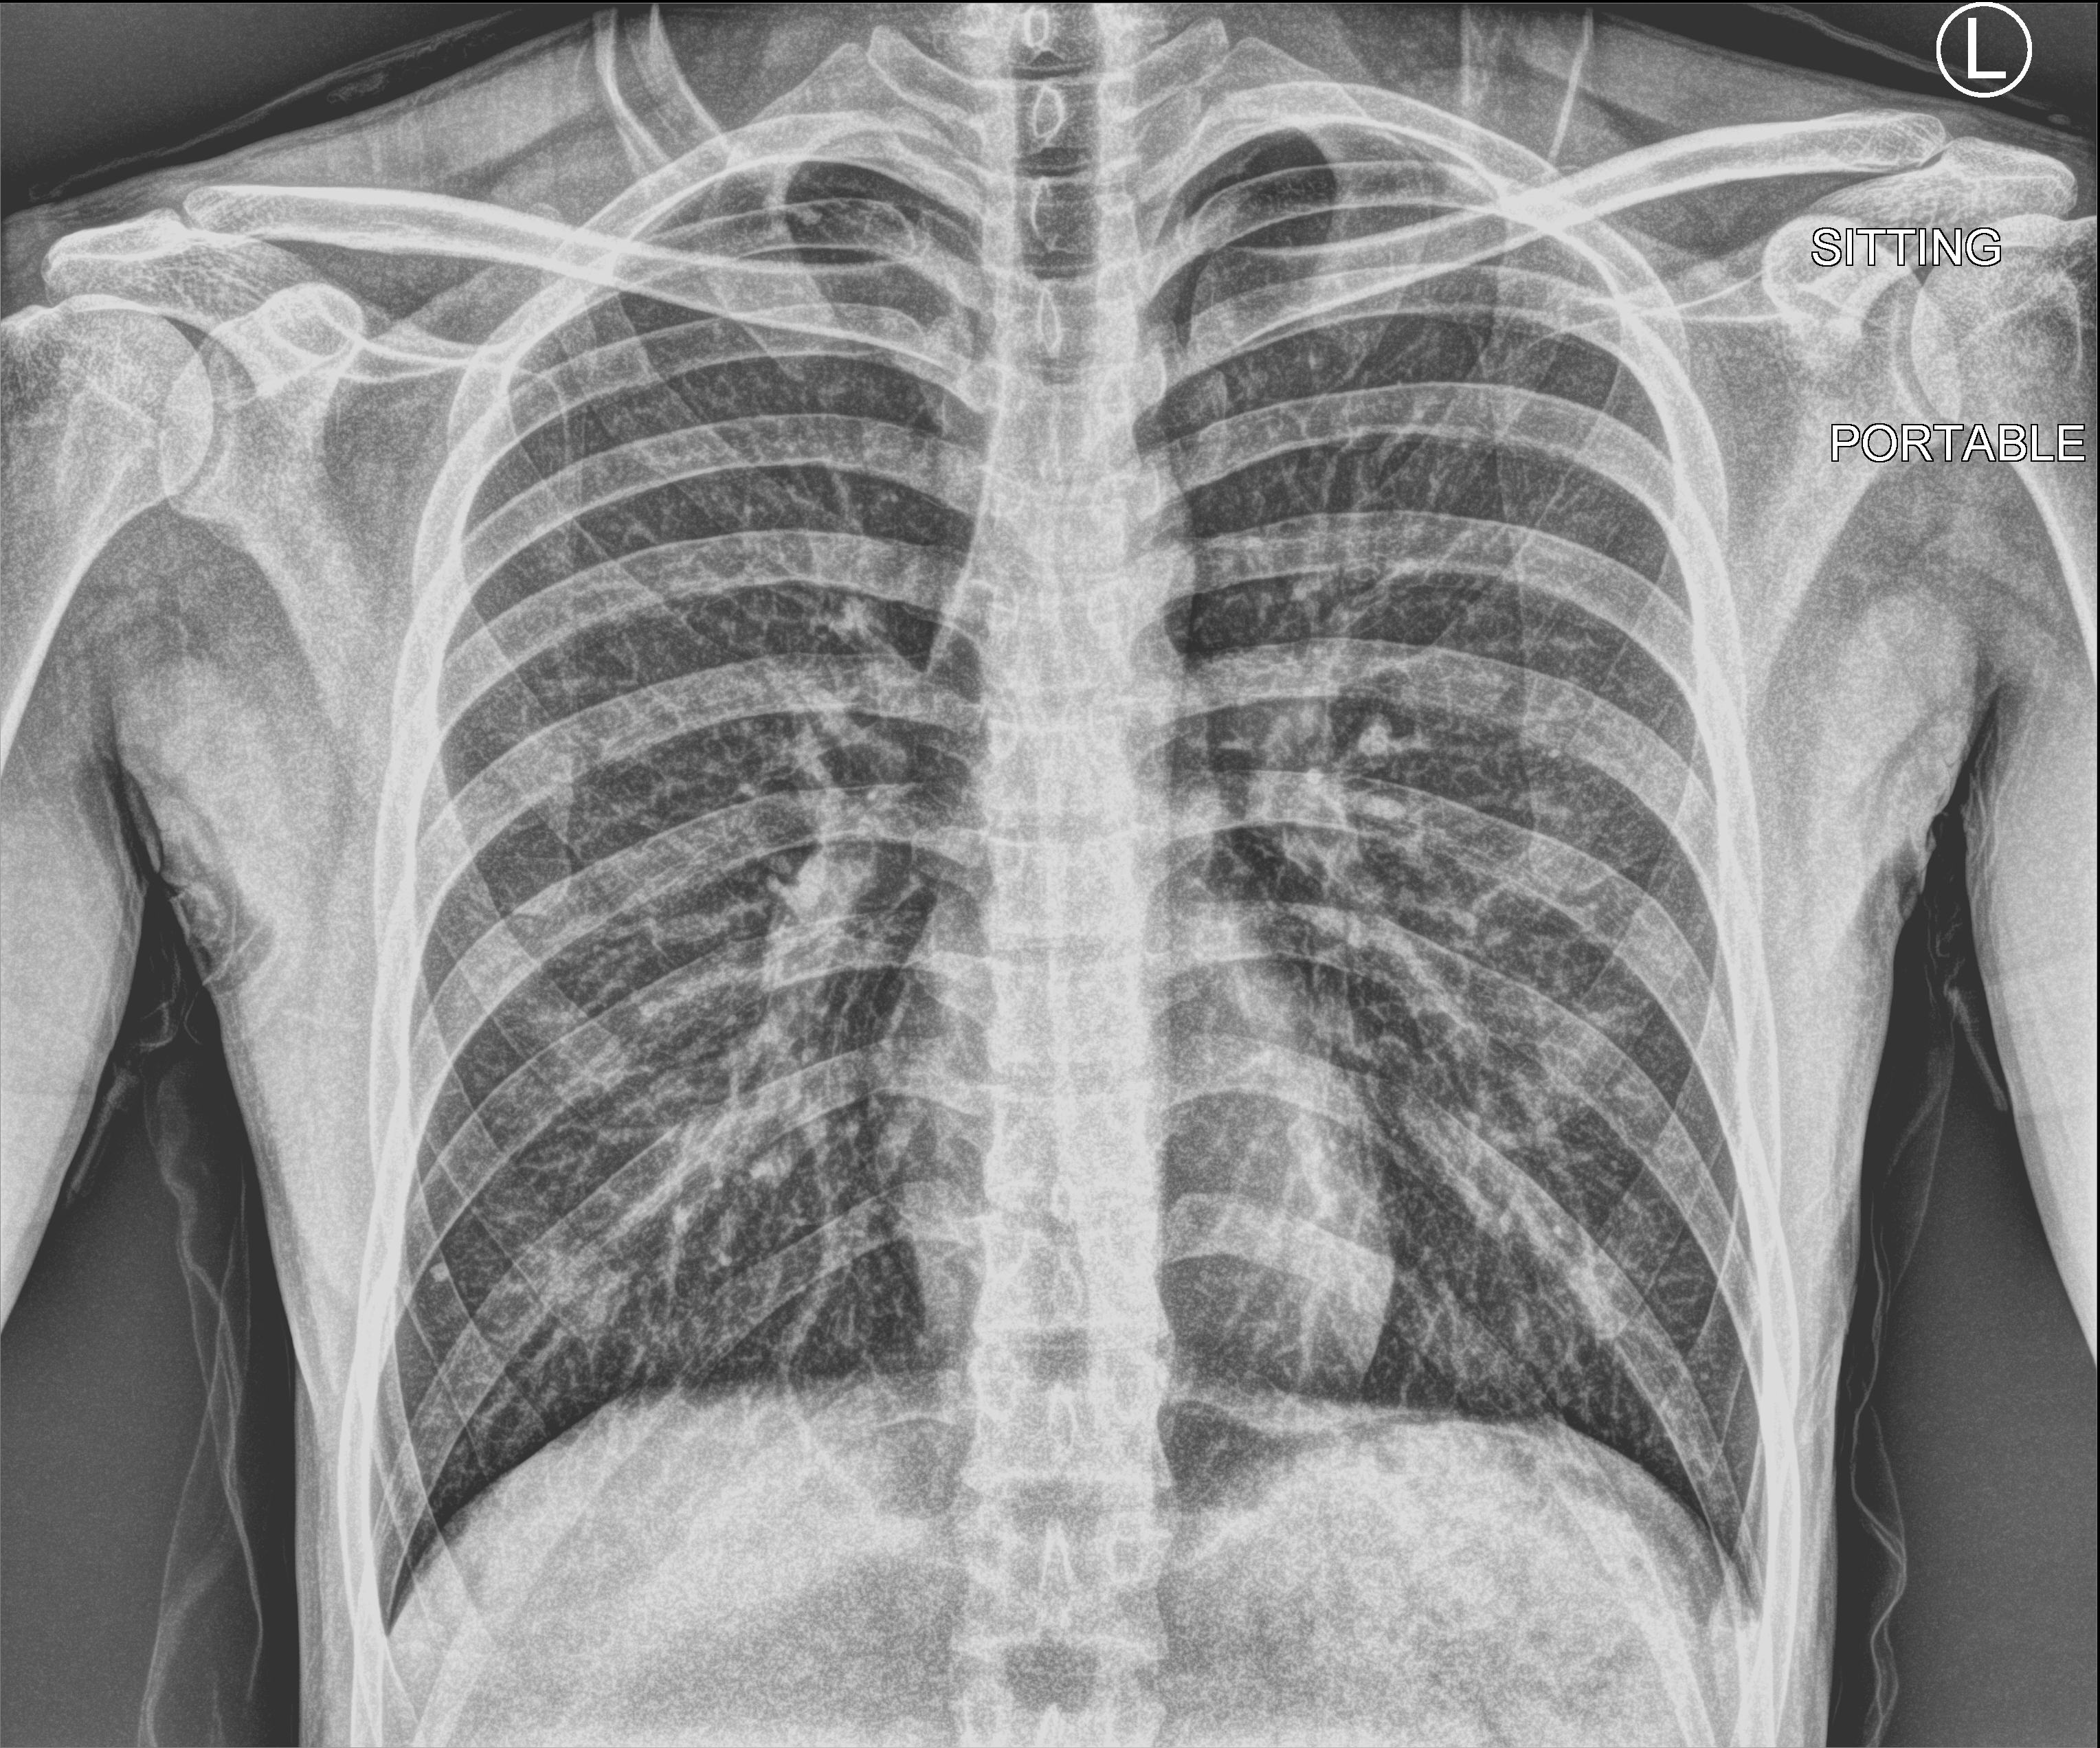
Portable chest radiograph. Patient hospitalised with COVID-19; male, aged 18–59 years.
Hospital-stay facts (about this admission, not read from this image; timing relative to this image not recorded): length of hospital stay: 1 day.